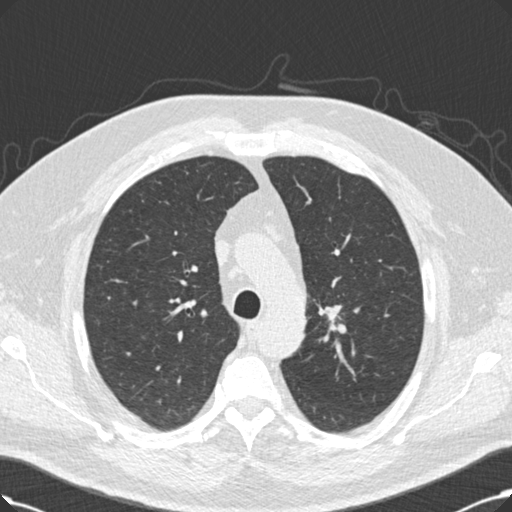
Low-dose screening chest CT, axial slice; third annual screen; lung window (W 1500 / L -600 HU); 2 mm slice thickness; standard (soft-tissue) reconstruction kernel (B30f). Male, age 60 years at enrolment. Current smoker at enrolment.
Expert reader's lesion annotation, bounding box [x1, y1, x2, y2] px = [318, 301, 351, 335]. Reader record for this screening exam (exam-level; its link to the box is not recorded): non-calcified nodule or mass ≥4 mm, left upper lobe, 20 × 20 mm, smooth margins, soft tissue attenuation, pre-existing on the prior screen: no. Lung cancer was diagnosed 53 days after this screen: squamous cell carcinoma, NOS, right upper lobe, 27 mm at pathology.